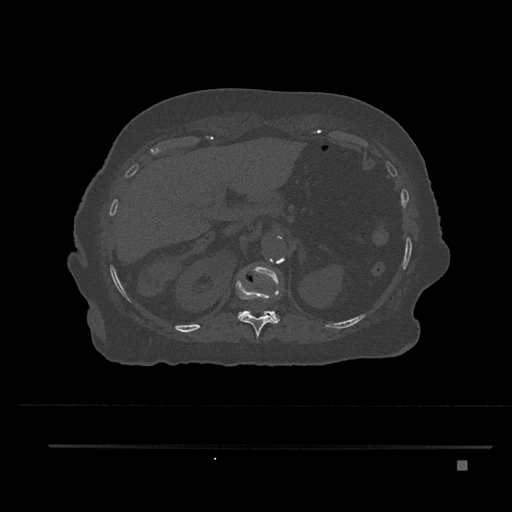
CT including the spine, one axial slice. 120 kVp. Bone window (W 1800 / L 400 HU). 0.5 mm slice thickness. 512 × 512 image matrix, field of view 437 × 437 mm. Female patient, age 76 years. Case-level facts recorded for this patient, not image findings: primary cancer: lung; vertebrae with lytic lesions (as recorded): T11, L3.
Outlined on this slice (semi-automatically segmented with operator editing):
- T11 vertebra: bounding box [x1, y1, x2, y2] px = [236, 278, 281, 338]
- T12 vertebra: [238, 267, 280, 323]